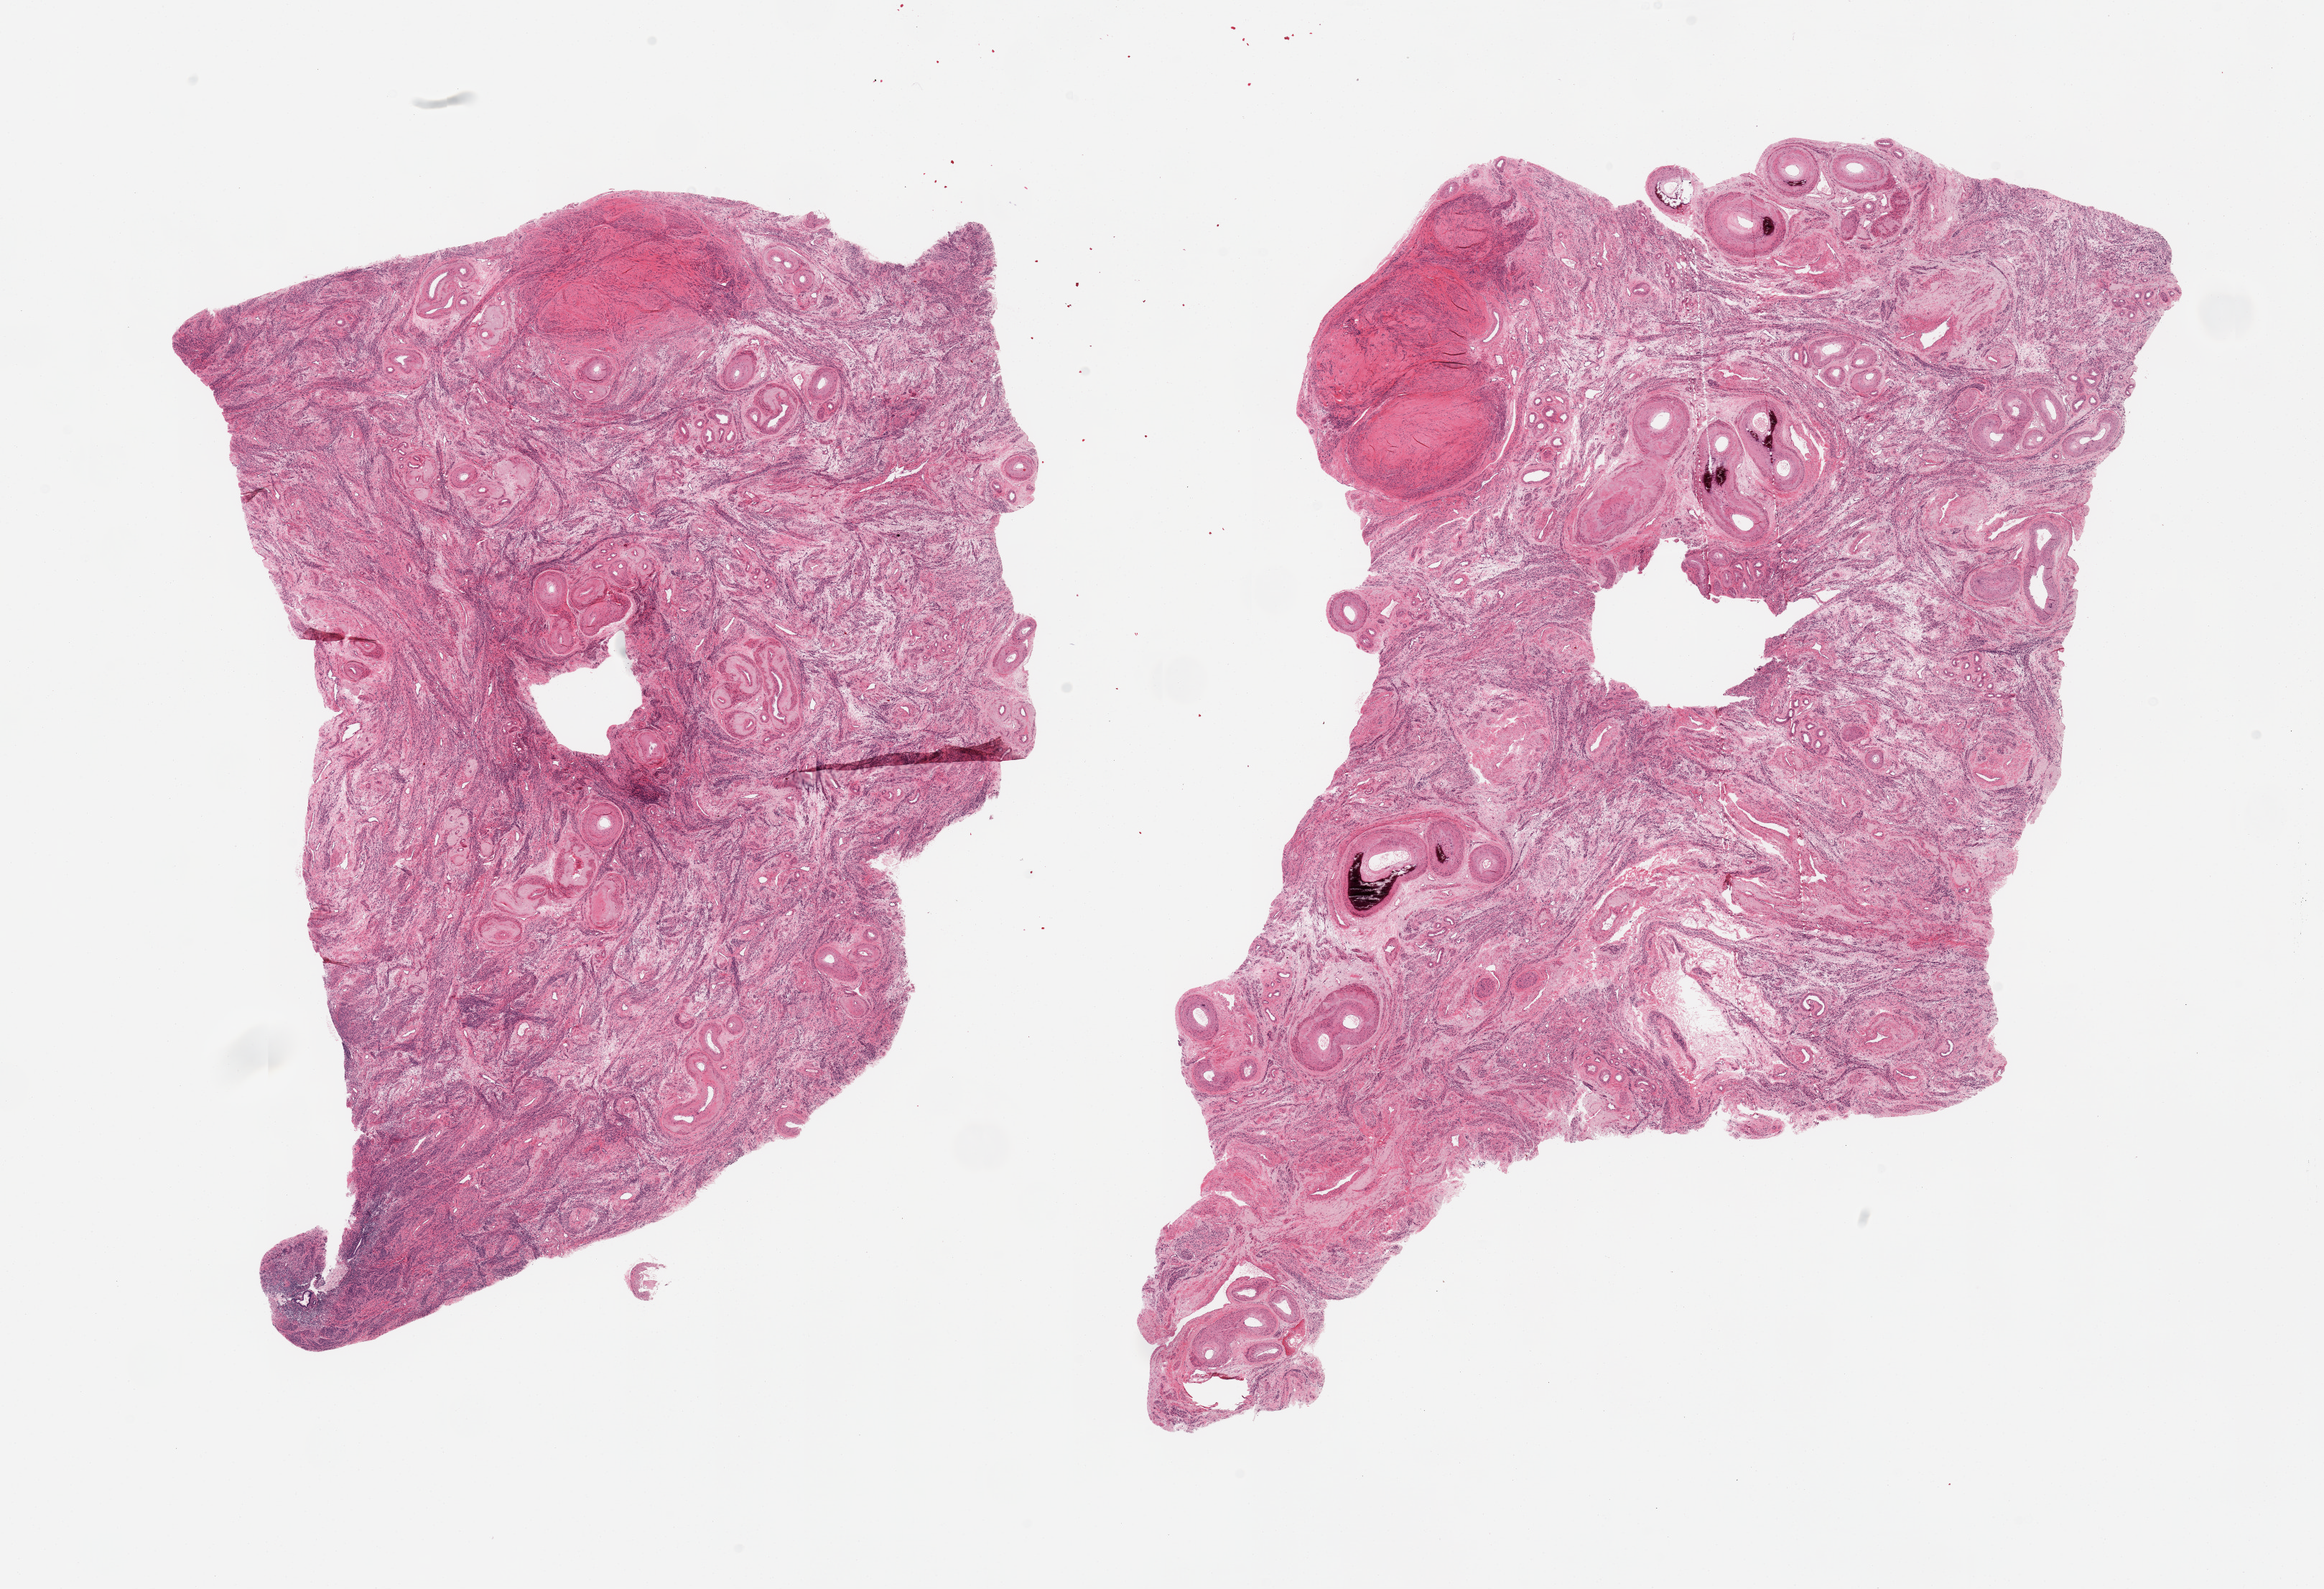
H&E whole-slide image, whole scanned area (about 25.6 x 17.5 mm, acquisition: 20x scan) shown as a low-resolution overview, PAXgene-fixed paraffin-embedded (PFPE) section, section of uterus (target tissue), tissue donor sample. Donor sex: female.
Pathologist's review note for this sample: 2 pieces, myometrium with hyalinizing small leiomyomata; minute focus of adenomyosis.